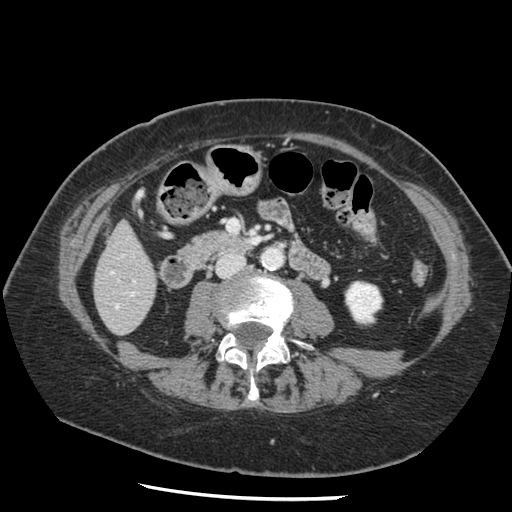
Contrast-enhanced abdominal CT, one axial slice; slice 33 of 148 in the series (ordered by position); 120 kVp; soft-tissue window (W 400 / L 40 HU); 2.5 mm slice thickness; 512 × 512 image matrix. Female patient, age 85 years. Case-level facts recorded for this patient, not image findings: diagnosis: colorectal cancer liver metastases, imaged before liver resection; multiple liver metastases: no; largest metastasis: 0.9 cm; disease in both lobes: no.
Outlined on this slice (expert manual segmentation):
- hepatic veins: bounding box <111,272,118,307> (left, top, right, bottom; pixels)
- liver: <95,224,156,334>
- planned liver remnant (the part of the liver to remain after resection): <95,224,156,331>